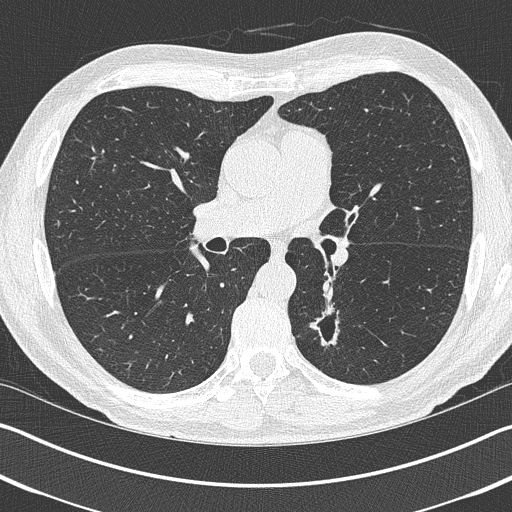
Low-dose screening chest CT, one axial slice; position 232 of 402 along the scan axis; reconstruction kernel B50f; lung window (W 1500 / L -600 HU); 512 × 512 image matrix.
Outlined on this slice (manually delineated by an expert):
- lesion 1 (tumor, lower lobe of left lung): bounding box <310,304,339,347> (left, top, right, bottom; pixels)